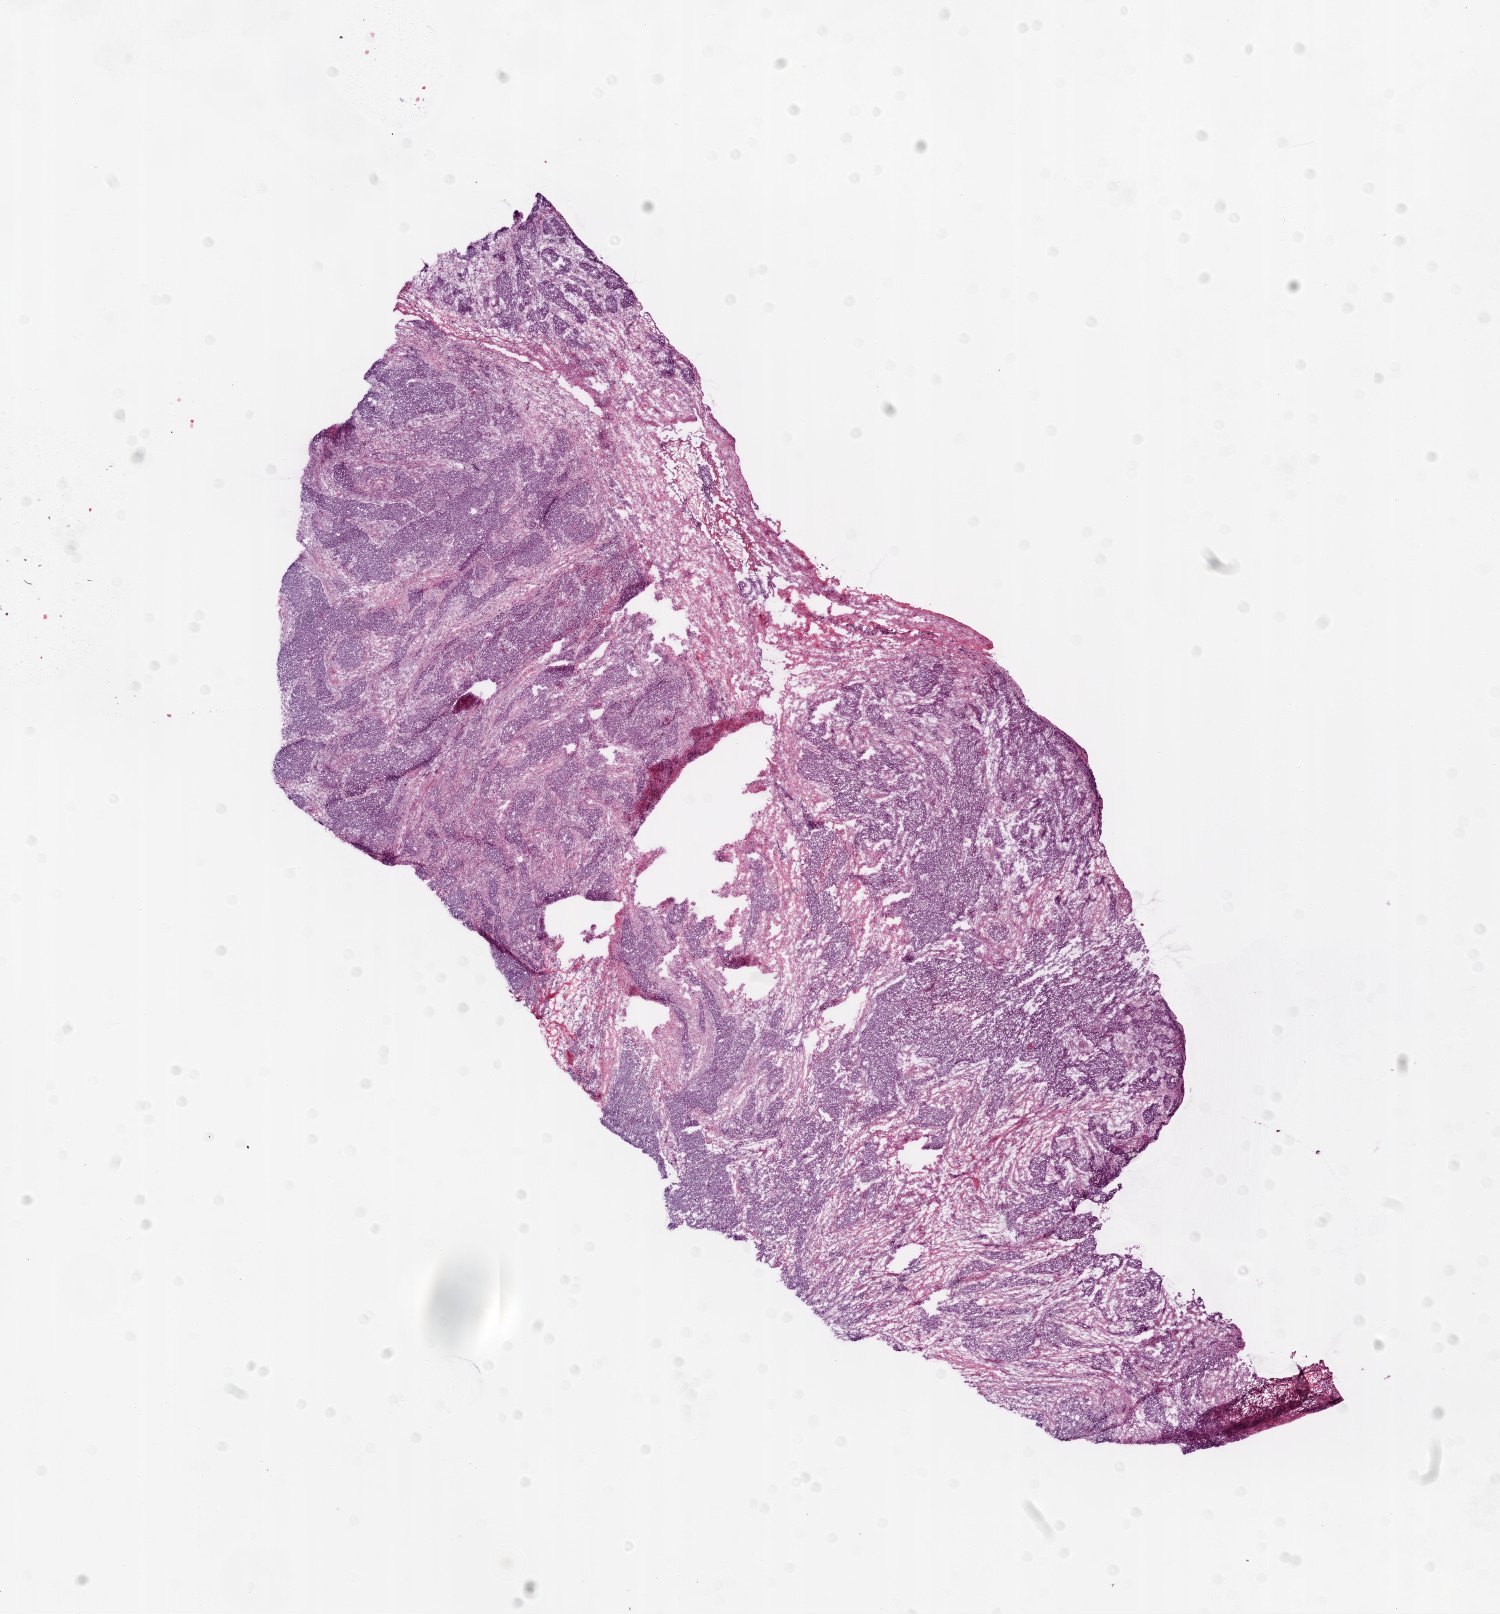
Digitized Hematoxylin and eosin (H&E) stained tissue section (whole slide) — whole scanned area (about 12.0 x 13.0 mm, slide scanned at 20x) shown as a low-resolution overview; frozen section from the bottom of the tissue portion; sample: primary tumour, ovary. Patient: female, age at initial diagnosis 46 years. Slide review estimates, as recorded: tumour cells 76%, tumour nuclei 90%.
Diagnosis: Serous cystadenocarcinoma, NOS.